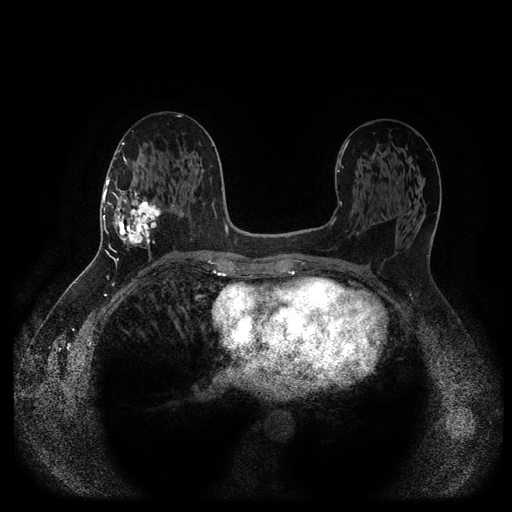
Breast MRI (dynamic contrast-enhanced, multi-phase), one axial slice; slice 51 of 116 in the series (ordered by position); dynamic contrast-enhanced series, time point 2 of 5 at this slice position (early post-contrast); 1.5 T; TE 2.6 ms, TR 5.3 ms; 2 mm slice thickness; 512 × 512 image matrix, field of view 360 × 360 mm. Female patient, age 58 years.
Outlined on this slice (semi-automatic segmentation, software-assisted and operator-edited):
- breast lesion (labelled 'tumour' in the annotation; benign lesions carry a separate 'benign' label): box from (x=113, y=187) to (x=163, y=251) px